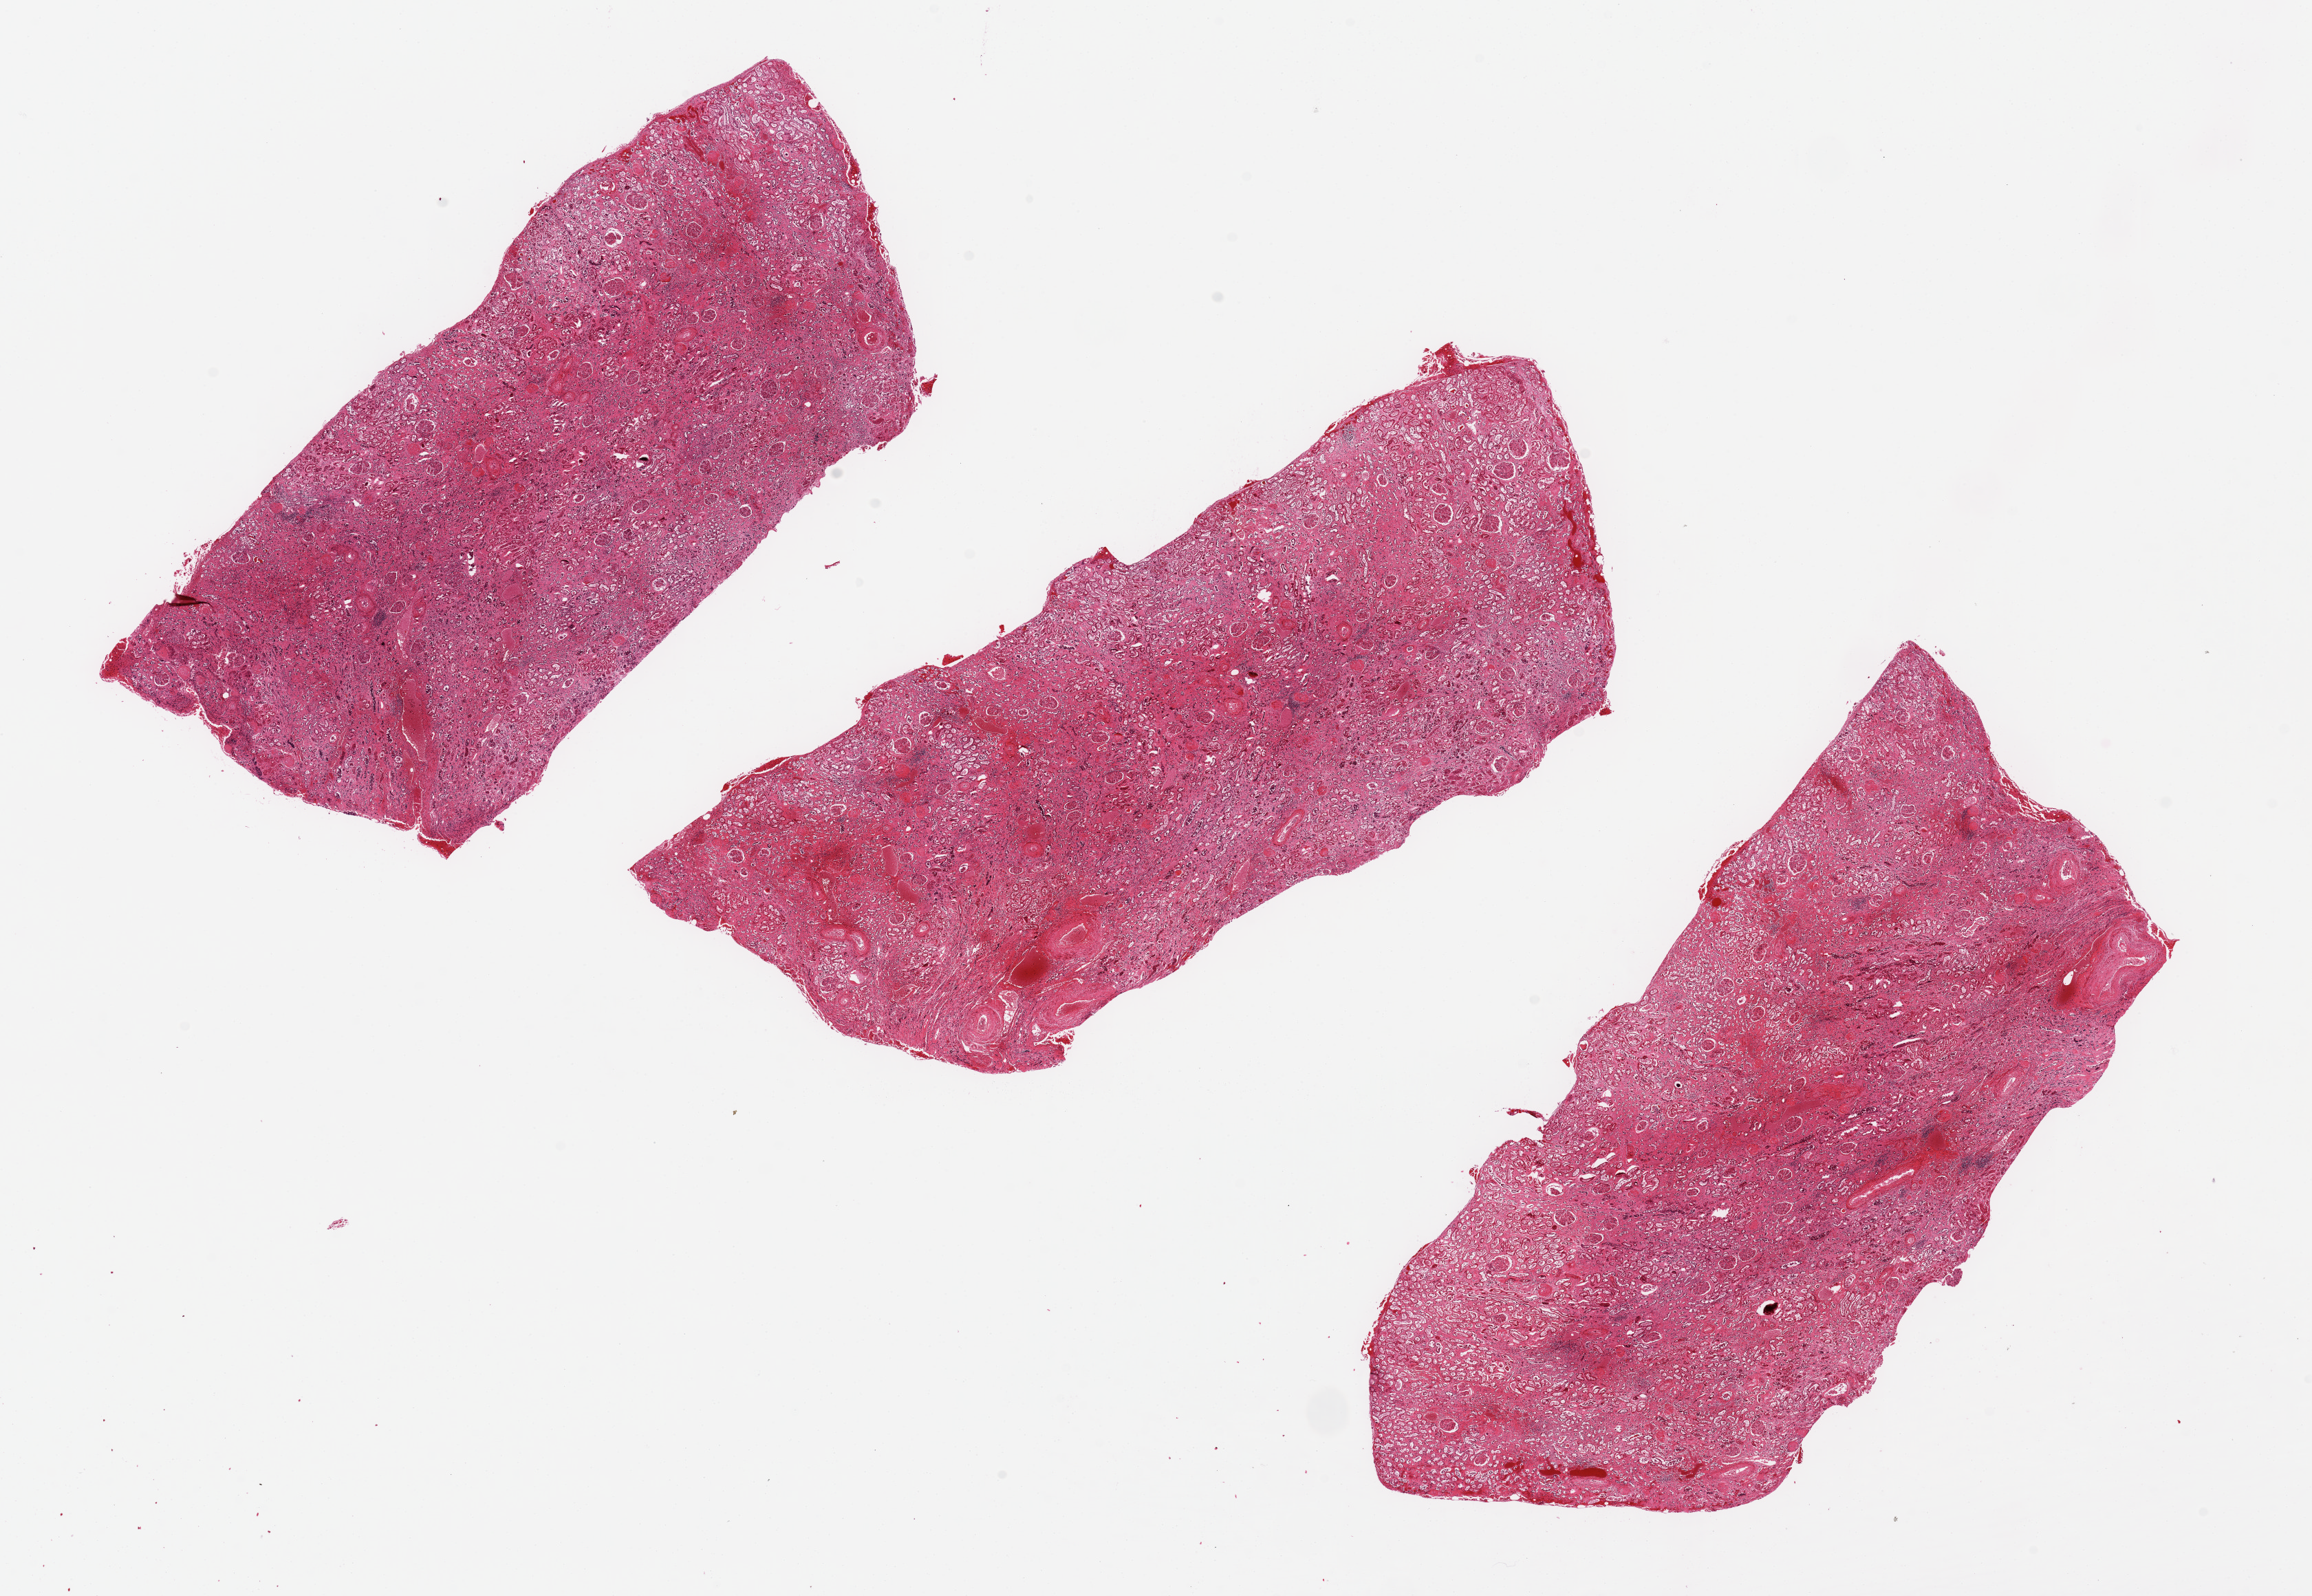
Hematoxylin and eosin (H&E) whole-slide image, brightfield — whole scanned area (about 26.6 x 18.3 mm) shown as a low-resolution overview, PAXgene-fixed paraffin-embedded (PFPE) section, section of renal cortex (target tissue), donor tissue sample. Male donor.
- review note (as recorded): Moderate autolysis of tubules. Moderate interstitial fibrosis/nephrosclerosis